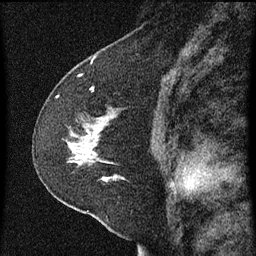
Breast MRI (dynamic contrast-enhanced), one sagittal slice; position 38 of 60 along the scan axis; dynamic contrast-enhanced series, image 2 of 3 at this slice position (ordered by acquisition); 1.5 T; TE 4.2 ms, TR 8 ms; 2 mm slice thickness; 256 × 256 image matrix, field of view 180 × 180 mm. Female patient, age 47 years.
Structures marked on this image (semi-automatically segmented with operator editing):
- analysis volume of interest (the breast-tissue region the enhancement analysis was run in; not a lesion): bounding box (x1, y1, x2, y2) in pixels: (36, 100, 158, 213)
- tumour enhancement mask (voxels above the 70 % enhancement threshold inside the analysis volume of interest): (72, 130, 107, 179)